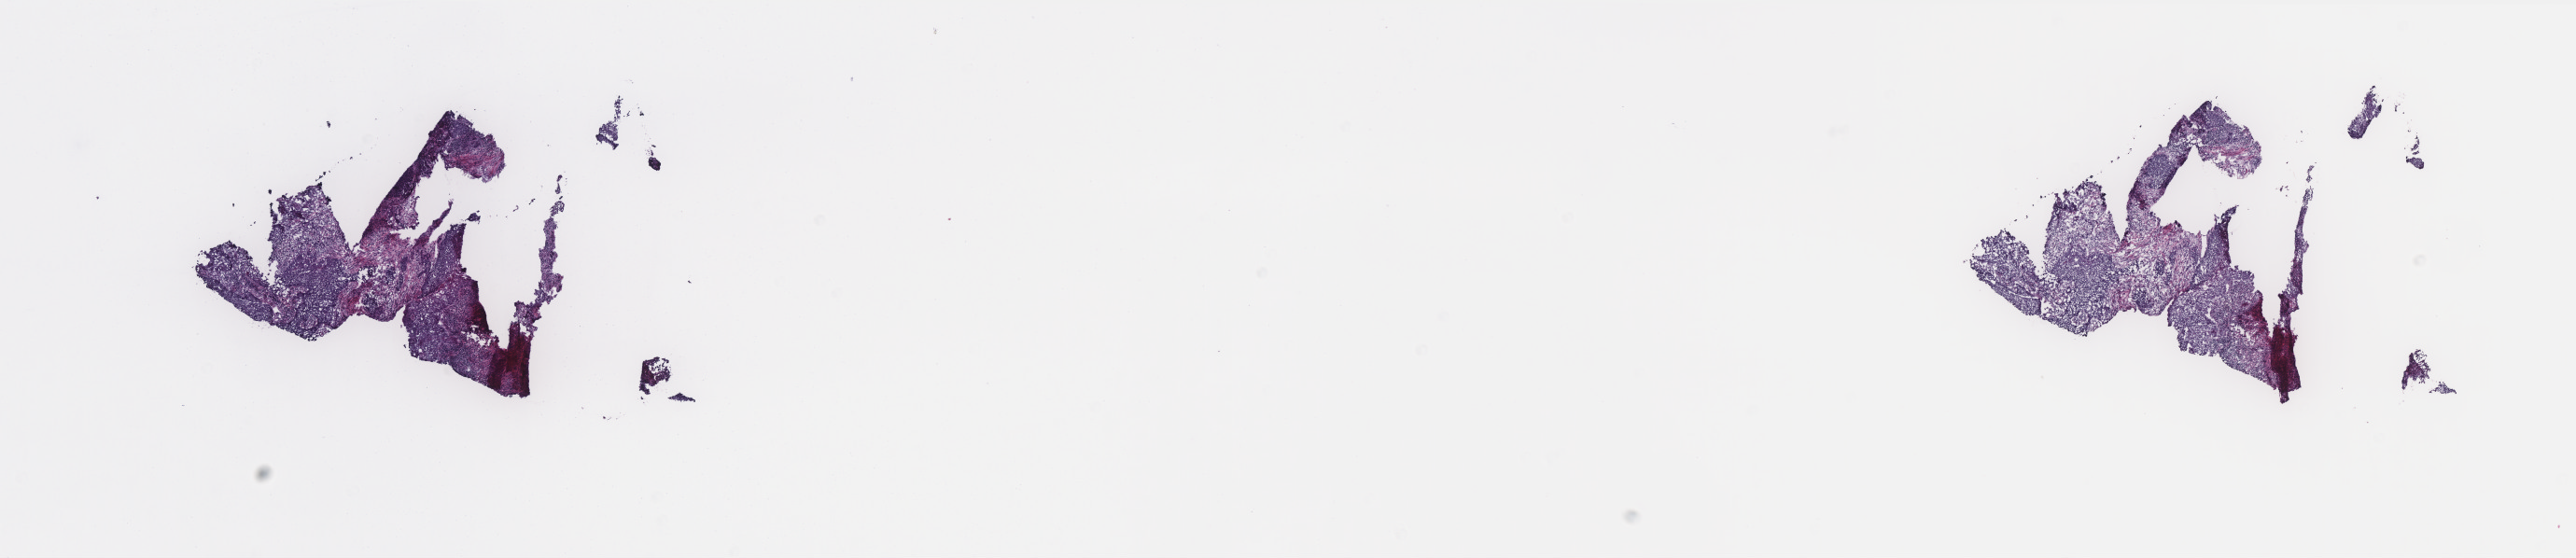
Hematoxylin and eosin (H&E) stained whole-slide image — a low-resolution overview of the entire scanned area, about 22.1 x 4.8 mm, frozen section from the top of the tissue portion, cervix, primary tumour sample. Female patient; age at initial diagnosis 64 years. Histologic grade: G2 (moderately differentiated). Composition of this section per pathologist review: tumour cells 60%, tumour nuclei 60%, normal cells 0%, stromal cells 40%, necrosis 0%. Inflammatory infiltration, as recorded: lymphocyte infiltration 15%, monocyte infiltration 0%, neutrophil infiltration 1%.
Diagnosis: Squamous cell carcinoma, large cell, nonkeratinizing, NOS (cervix uteri). Lymph nodes positive (case pathology): 2 of 38 examined. FIGO stage: IB2.